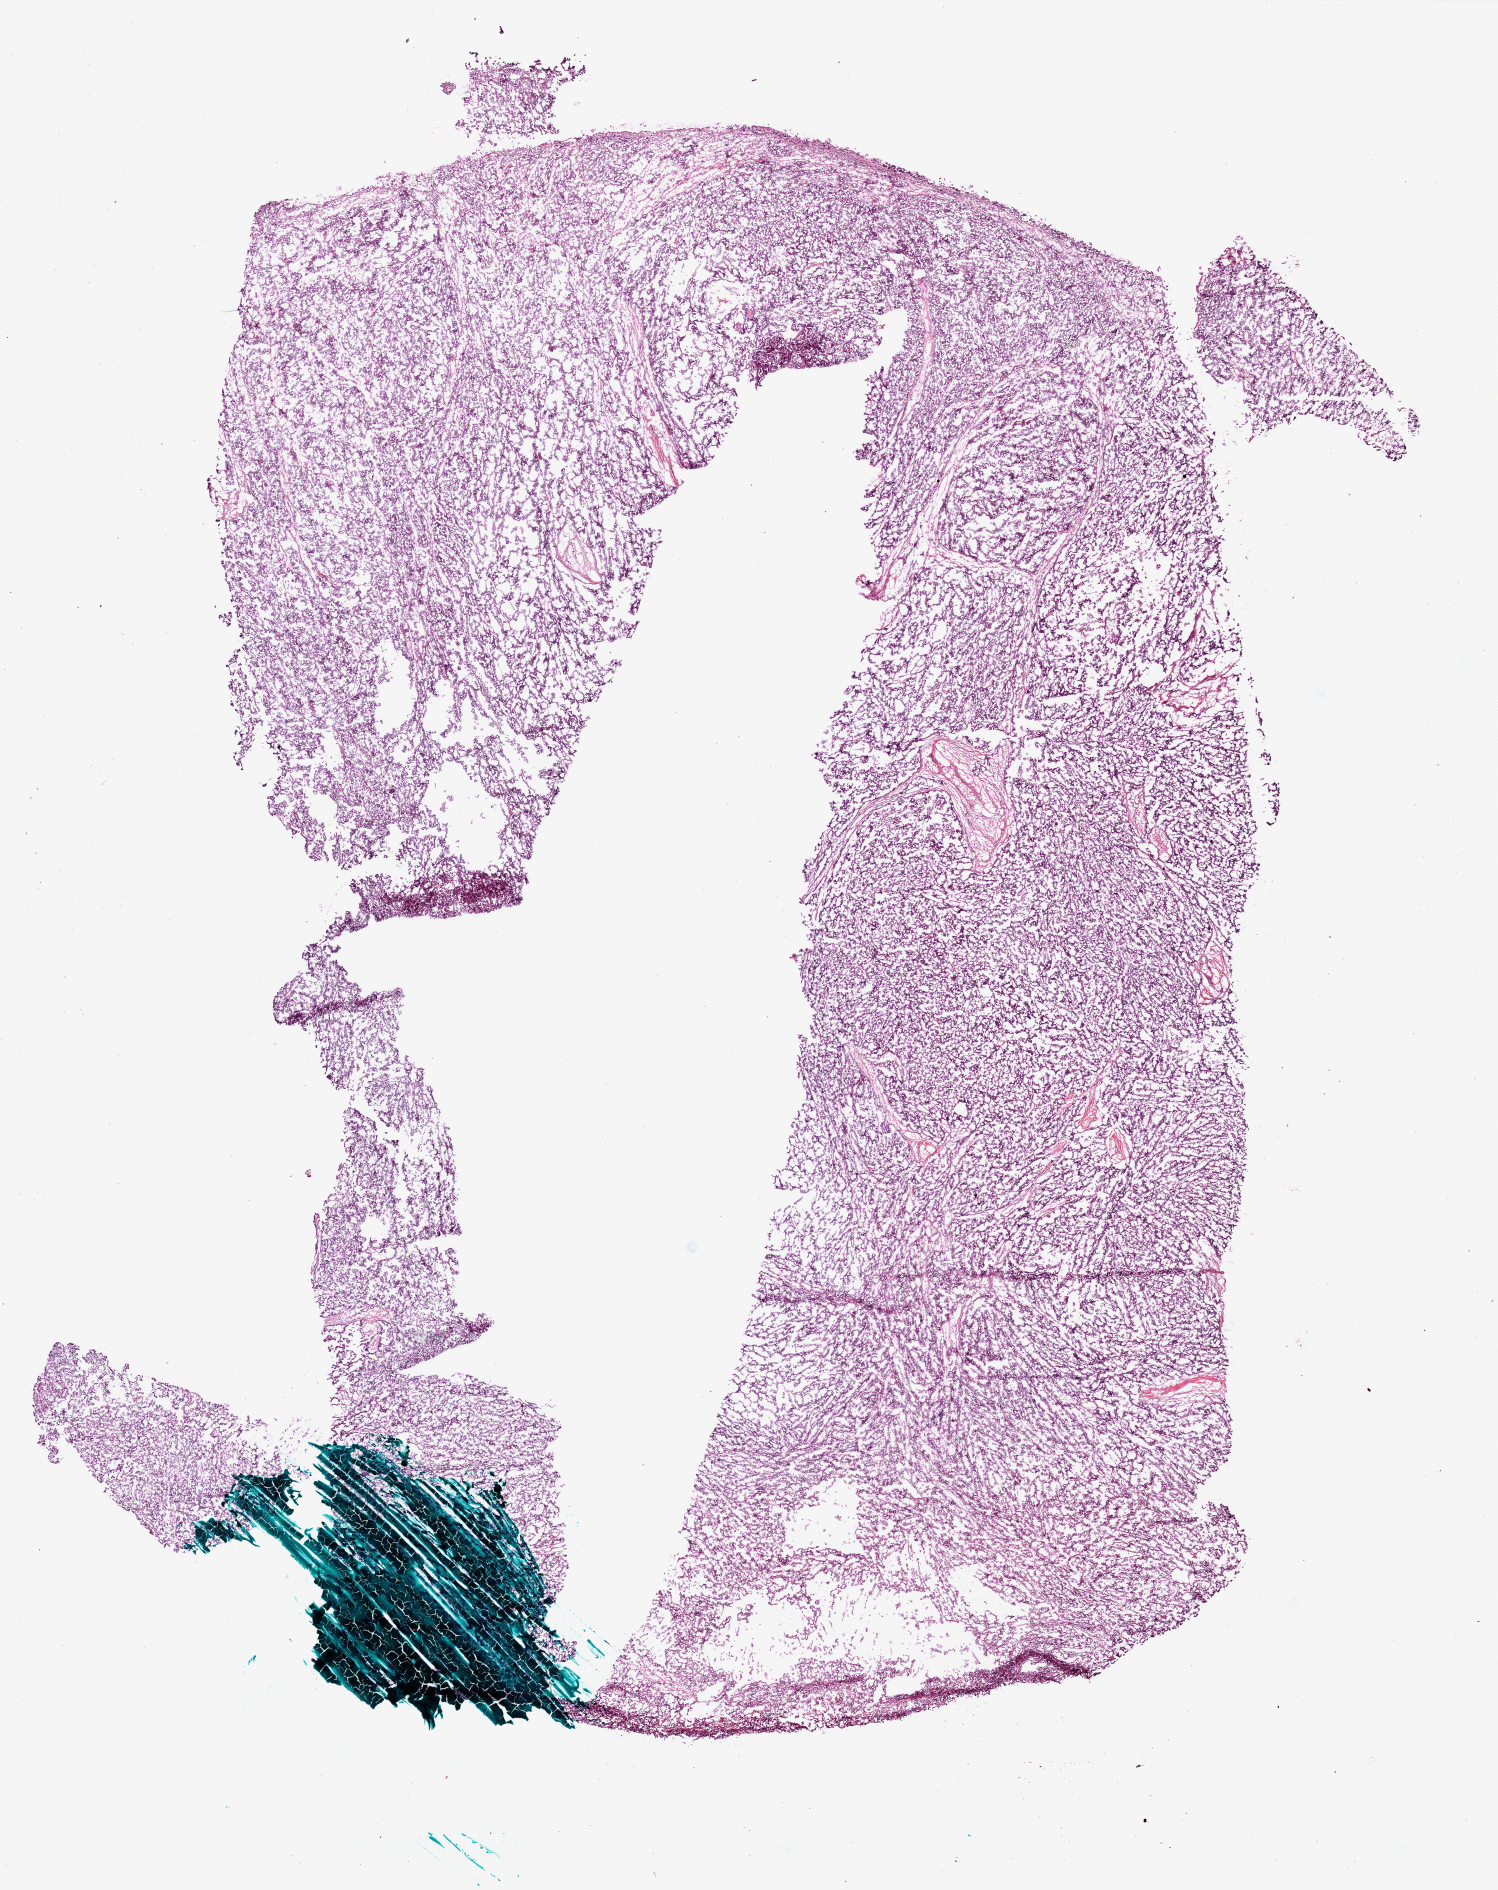
Digitized Hematoxylin and eosin (H&E) stained tissue section (whole slide), shown as a low-resolution overview of the whole scanned area (about 12.0 x 15.2 mm). Frozen section from the bottom of the tissue portion. Ovary, primary tumour sample. Female patient; age at initial diagnosis 66 years. Histologic grade: G3 (poorly differentiated). Pathologist review of this section (percent, as recorded): tumour cells 95%, tumour nuclei 98%, normal cells 0%, stromal cells 5%, necrosis 0%.
FIGO stage: IIIC. Diagnosis: Serous cystadenocarcinoma, NOS. Laterality: bilateral.